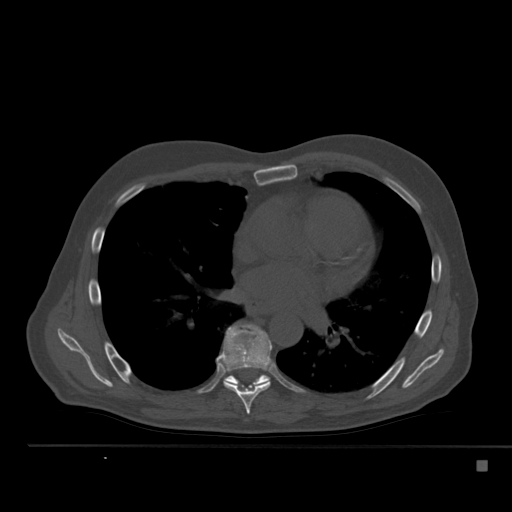
CT including the spine, one axial slice; position 321 of 517 along the scan axis; reconstruction kernel Br40s; bone window (W 1800 / L 400 HU); 1.5 mm slice thickness; 512 × 512 image matrix, field of view 408 × 408 mm. Patient: male, 70 years. Case-level facts recorded for this patient, not image findings: primary cancer: renal.
Annotated regions visible in this slice (semi-automatic segmentation, software-assisted and operator-edited):
- T7 vertebra: bounding box (x1, y1, x2, y2) in pixels: (220, 324, 272, 414)
- T8 vertebra: (224, 374, 270, 390)